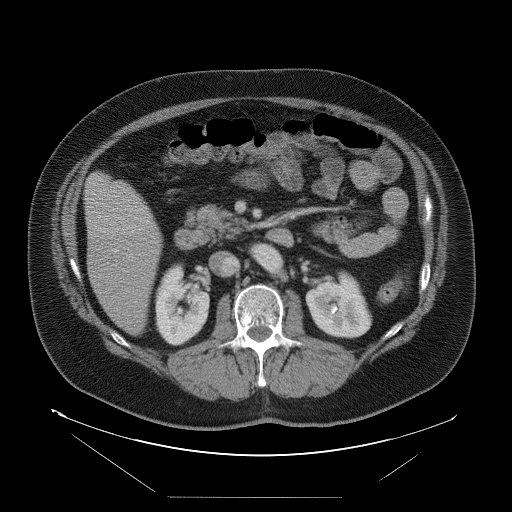
Contrast-enhanced abdominal CT, one axial slice; position 35 of 114 along the scan axis; intravenous contrast given; soft-tissue window (W 400 / L 40 HU); 512 × 512 image matrix. Male patient, age 61 years. Case-level facts recorded for this patient, not image findings: diagnosis: colorectal cancer liver metastases, imaged before liver resection; multiple liver metastases: no.
Structures marked on this image (outlined manually by an expert reader):
- liver: bounding box (x1, y1, x2, y2) in pixels: (85, 174, 163, 335)